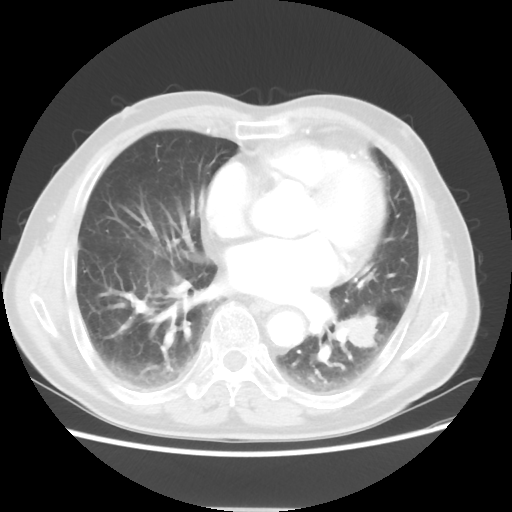
Chest CT, one axial slice; reconstruction kernel STANDARD; lung window (W 1500 / L -600 HU); 5 mm slice thickness; 512 × 512 image matrix, field of view 366 × 366 mm. Patient: male, 71 years. Case-level facts recorded for this patient, not image findings: clinical TNM (as recorded): T1c N1 M0.
Annotated regions visible in this slice (bounding box drawn by a radiologist):
- lung tumour (recorded histology: adenocarcinoma): bounding box (x1, y1, x2, y2) in pixels: (336, 303, 383, 360)